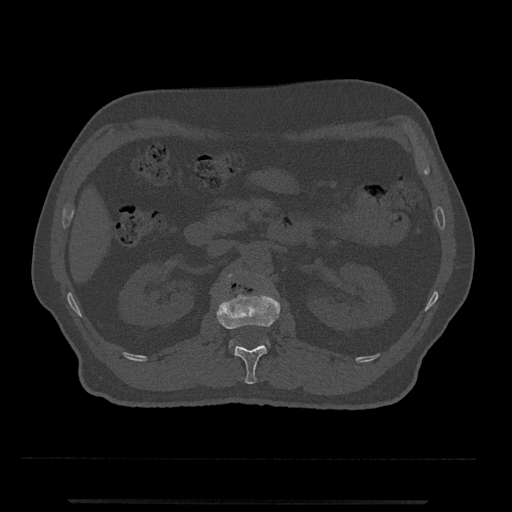
CT including the spine, one axial slice; position 313 of 797 along the scan axis; bone window (W 1800 / L 400 HU); 0.5 mm slice thickness; 512 × 512 image matrix, field of view 419 × 419 mm. Male patient, age 63 years. Case-level facts recorded for this patient, not image findings: primary cancer: prostate.
Structures marked on this image (semi-automatically segmented with operator editing):
- L1 vertebra: bounding box [x1, y1, x2, y2] px = [217, 291, 280, 384]
- L2 vertebra: [227, 274, 269, 348]